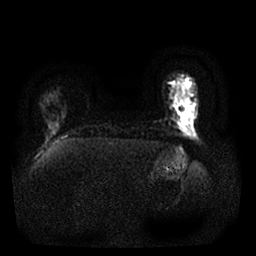
Breast MRI, one axial slice. Position 4 of 25 along the scan axis. Diffusion-weighted series; image 2 of 4 stored at this slice position (different b-values; order by instance number). 1.5 T. 4 mm slice thickness. 256 × 256 image matrix, field of view 290 × 290 mm. Female patient.
Annotated regions visible in this slice (expert manual segmentation):
- tumour on diffusion-weighted imaging: bounding box <177,95,189,116> (left, top, right, bottom; pixels)